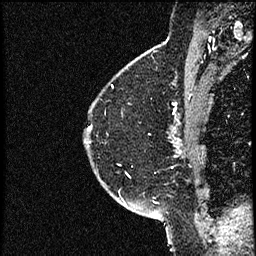
Breast MRI (dynamic contrast-enhanced), one sagittal slice. Position 42 of 52 along the scan axis. Dynamic contrast-enhanced study with each time point stored as its own series, time point 2 of 3 at this slice position (early post-contrast, ordered by acquisition time). 1.5 T. TE 4.2 ms, TR 17.6 ms. 2 mm slice thickness. 256 × 256 image matrix, field of view 200 × 200 mm. Patient: female, 49 years. From the clinical record (not read from this slice): setting: breast cancer imaged before/during neoadjuvant chemotherapy; receptor status: HER2-positive.
Annotated regions visible in this slice (semi-automatically segmented with operator editing):
- analysis volume of interest (the breast-tissue region the enhancement analysis was run in; not a lesion): box from (x=85, y=65) to (x=182, y=175) px
- tumour enhancement mask (voxels above the 100 % enhancement threshold inside the analysis volume of interest): (x=173, y=103)–(x=178, y=144)